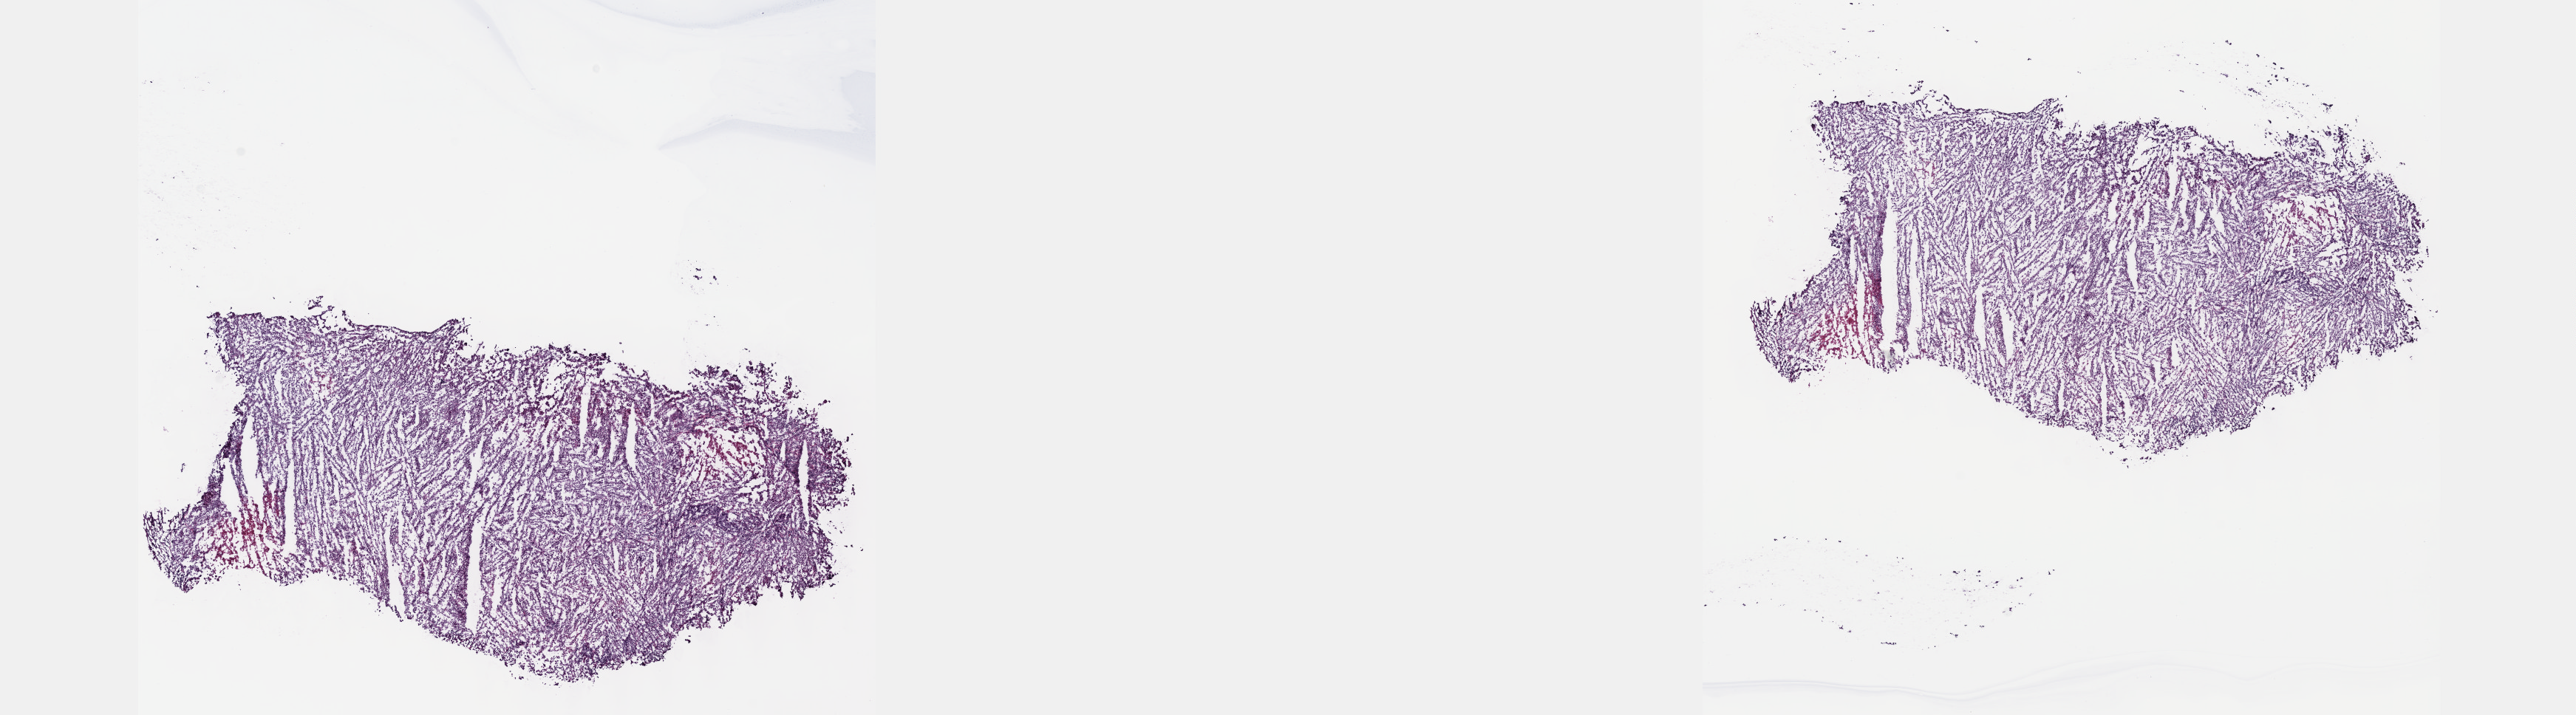
Digitized Hematoxylin and eosin (H&E) stained tissue section (whole slide) — shown as a low-resolution overview of the whole scanned area (about 28.2 x 7.8 mm). Frozen section from the top of the tissue portion. Metastatic tumour sample, sampled site not recorded. Male, age 52 years at initial diagnosis.
This section: metastatic tumour tissue. Patient diagnosis: Malignant melanoma, NOS.